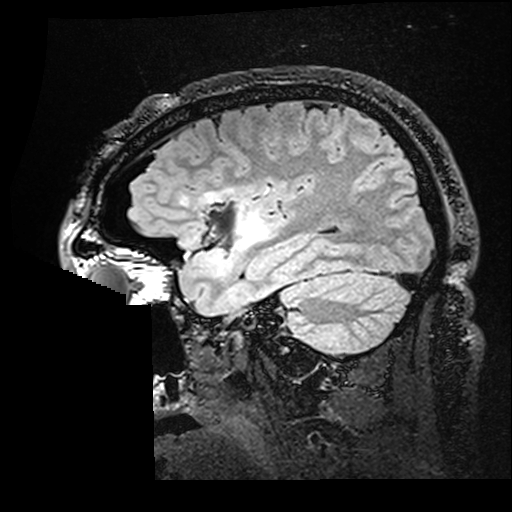
Brain MRI from a brain-tumour surgery series, one sagittal slice. Slice 123 of 176 in the series (ordered by position). T2 FLAIR. 1 mm slice thickness. 512 × 512 image matrix. From the clinical record (not read from this slice): histopathology: Astrocytoma; WHO grade: 2; IDH mutation: yes; tumour location: Right Insular.
Structures marked on this image (expert manual segmentation):
- residual tumour: bounding box <182,191,267,249> (left, top, right, bottom; pixels)